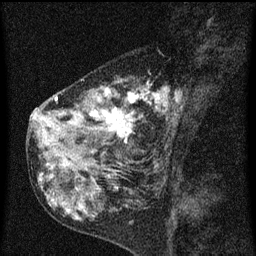
Breast MRI (dynamic contrast-enhanced), one sagittal slice. Slice 25 of 60 in the series (ordered by position). Dynamic contrast-enhanced series, image 2 of 3 at this slice position (ordered by acquisition). 1.5 T. TE 4.2 ms, TR 8 ms. 2 mm slice thickness. 256 × 256 image matrix. Female patient, age 55 years.
Outlined on this slice (semi-automatic segmentation, software-assisted and operator-edited):
- analysis volume of interest (the breast-tissue region the enhancement analysis was run in; not a lesion): bounding box <42,74,185,155> (left, top, right, bottom; pixels)
- tumour enhancement mask (voxels above the 70 % enhancement threshold inside the analysis volume of interest): <56,86,182,145>